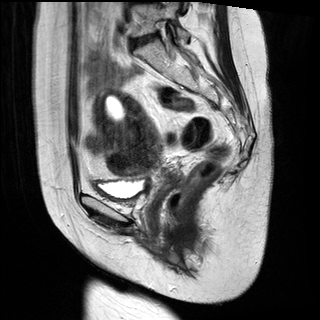
Pelvic MRI for cervical cancer, one sagittal slice. Position 16 of 28 along the scan axis. T2-weighted. 1.5 T. TE 89 ms, TR 2740 ms. 4 mm slice thickness. 320 × 320 image matrix. Female patient, age 49 years.
Outlined on this slice (expert manual segmentation):
- uterus and cervix: bounding box [x1, y1, x2, y2] px = [93, 89, 172, 192]